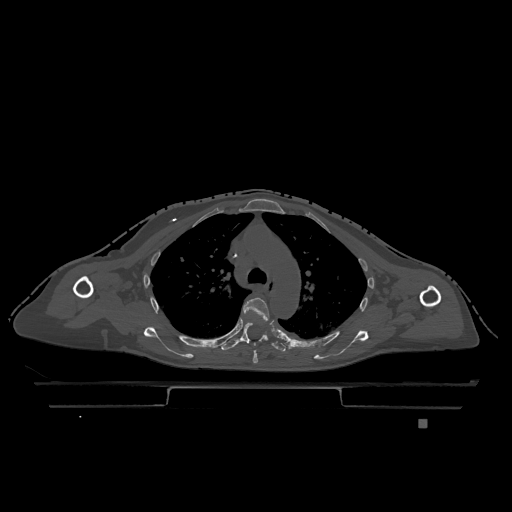
CT including the spine, one axial slice. Slice 856 of 1317 in the series (ordered by position). Bone window (W 1800 / L 400 HU). 0.5 mm slice thickness. 512 × 512 image matrix. Female patient, age 74 years. Case-level facts recorded for this patient, not image findings: primary cancer: lung.
Annotated regions visible in this slice (semi-automatically segmented with operator editing):
- T4 vertebra: bounding box (x1, y1, x2, y2) in pixels: (241, 297, 270, 363)
- T5 vertebra: (221, 322, 286, 353)